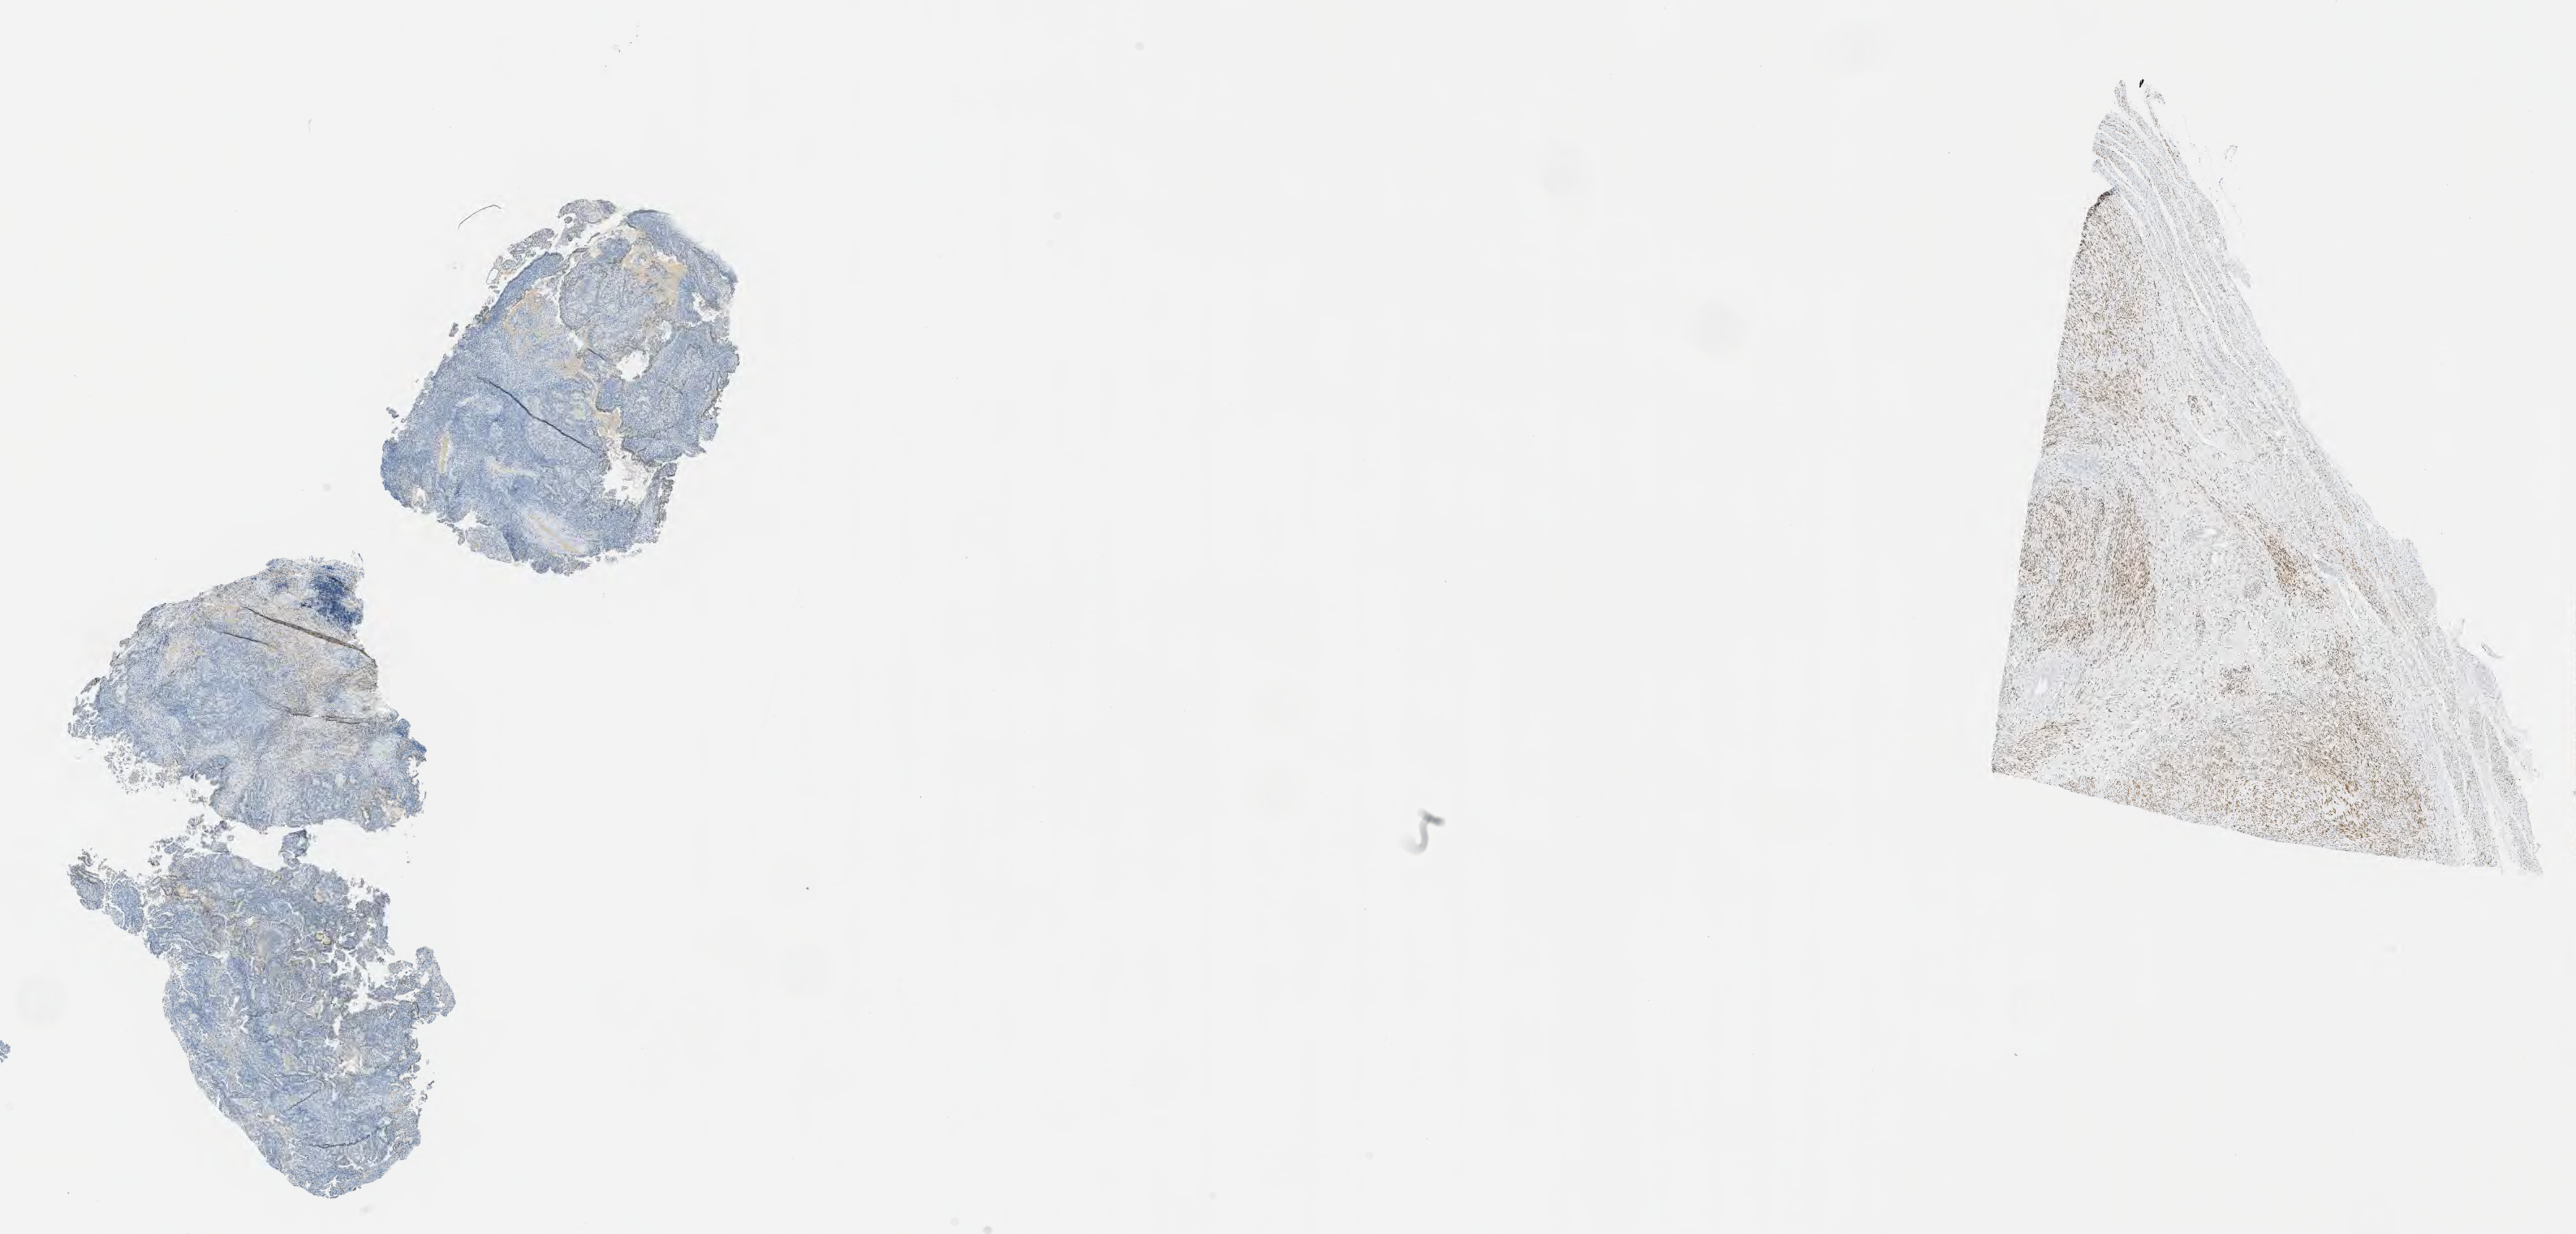
Immunohistochemistry (IHC) whole-slide image stained for progesterone receptor (PR), shown as a low-resolution overview of the whole scanned area (about 25.7 x 12.3 mm); specimen: tumor tissue; anatomic site: cervix. Patient: female, age 48 years.
* histologic diagnosis: Adenocarcinoma, NOS